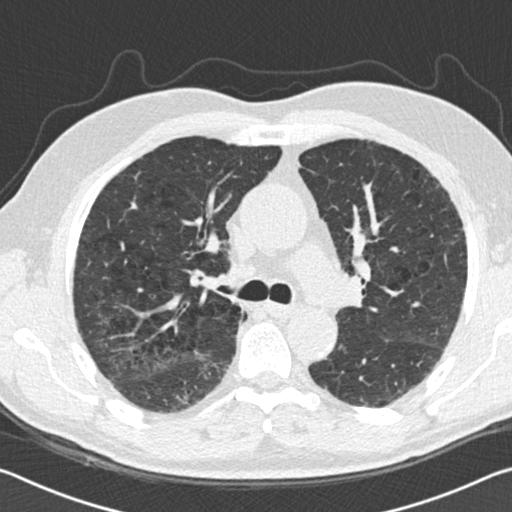
Low-dose screening chest CT, one axial slice. Position 88 of 142 along the scan axis. 120 kVp. Lung window (W 1500 / L -600 HU). 2 mm slice thickness. 512 × 512 image matrix, field of view 340 × 340 mm.
Structures marked on this image (manually delineated by an expert):
- lesion 1 (tumor, lower lobe of right lung): box from (x=176, y=392) to (x=188, y=404) px